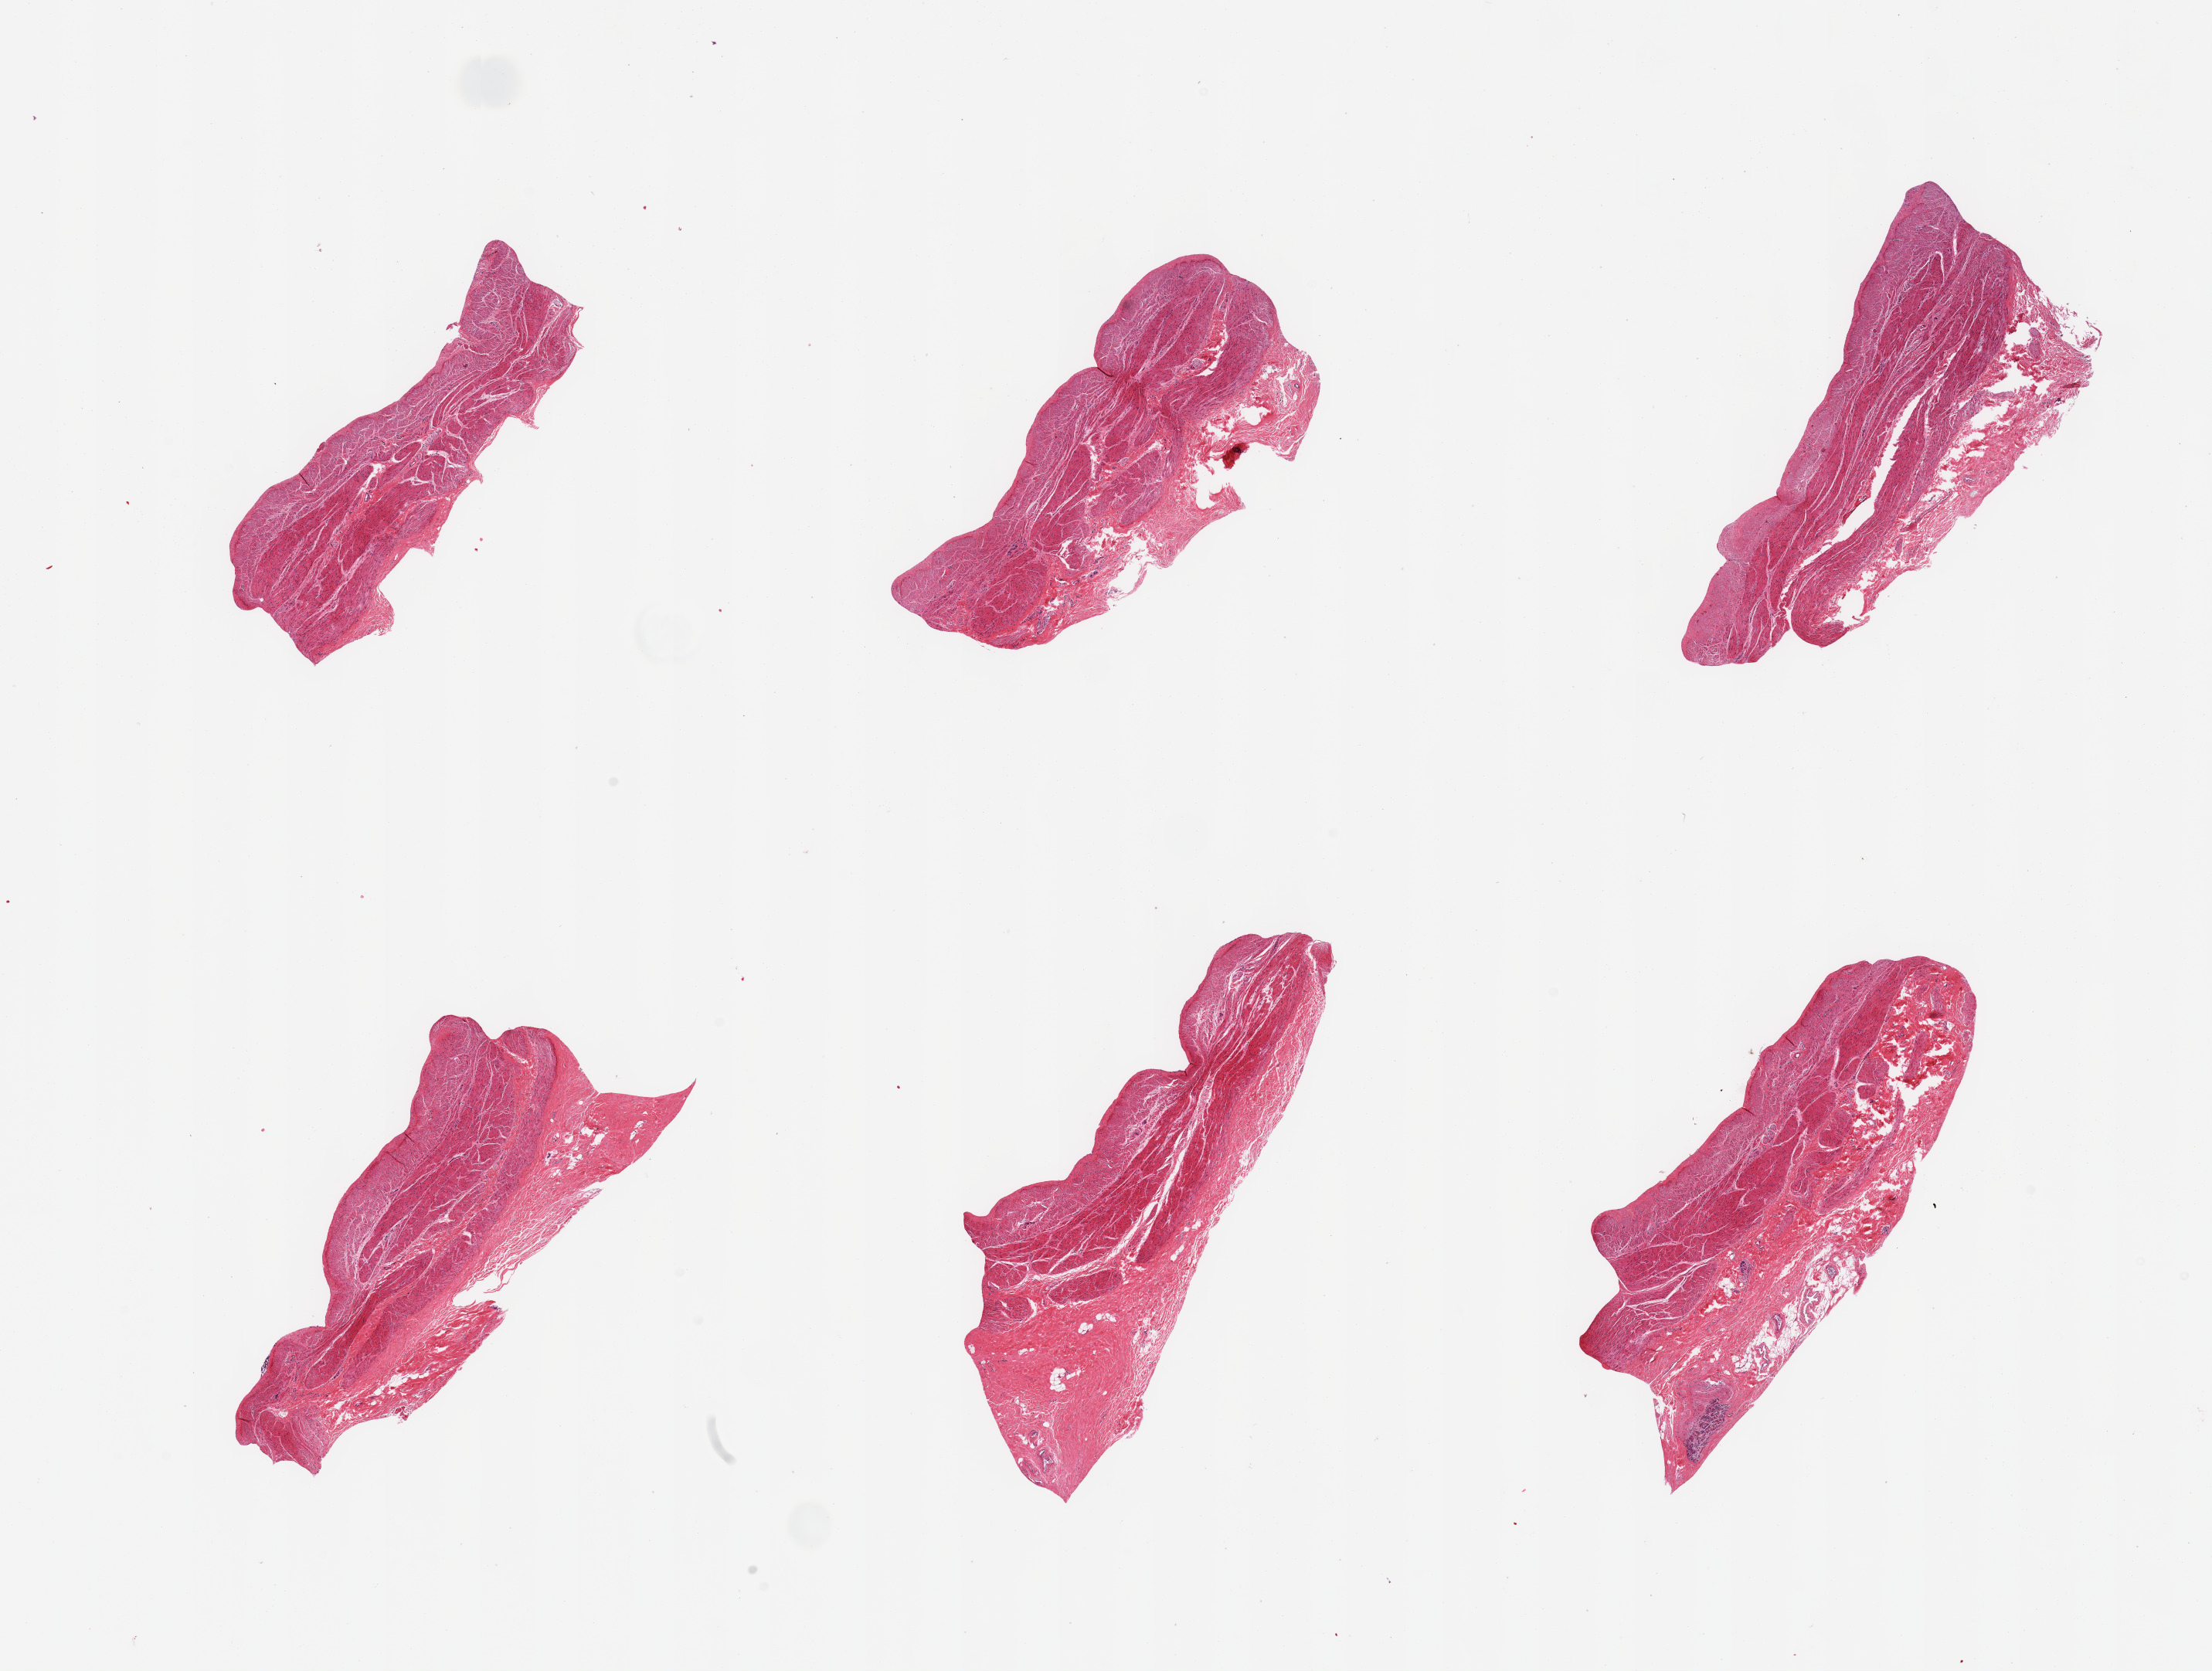
H&E whole-slide image — whole scanned area (about 22.6 x 17.1 mm, acquisition: 20x scan) shown as a low-resolution overview. PAXgene-fixed, paraffin-embedded tissue. Target tissue: sigmoid colon. Tissue donor sample. Male donor.
Pathologist's review note for this sample: 6 pieces; muscularis propria & submucosa.